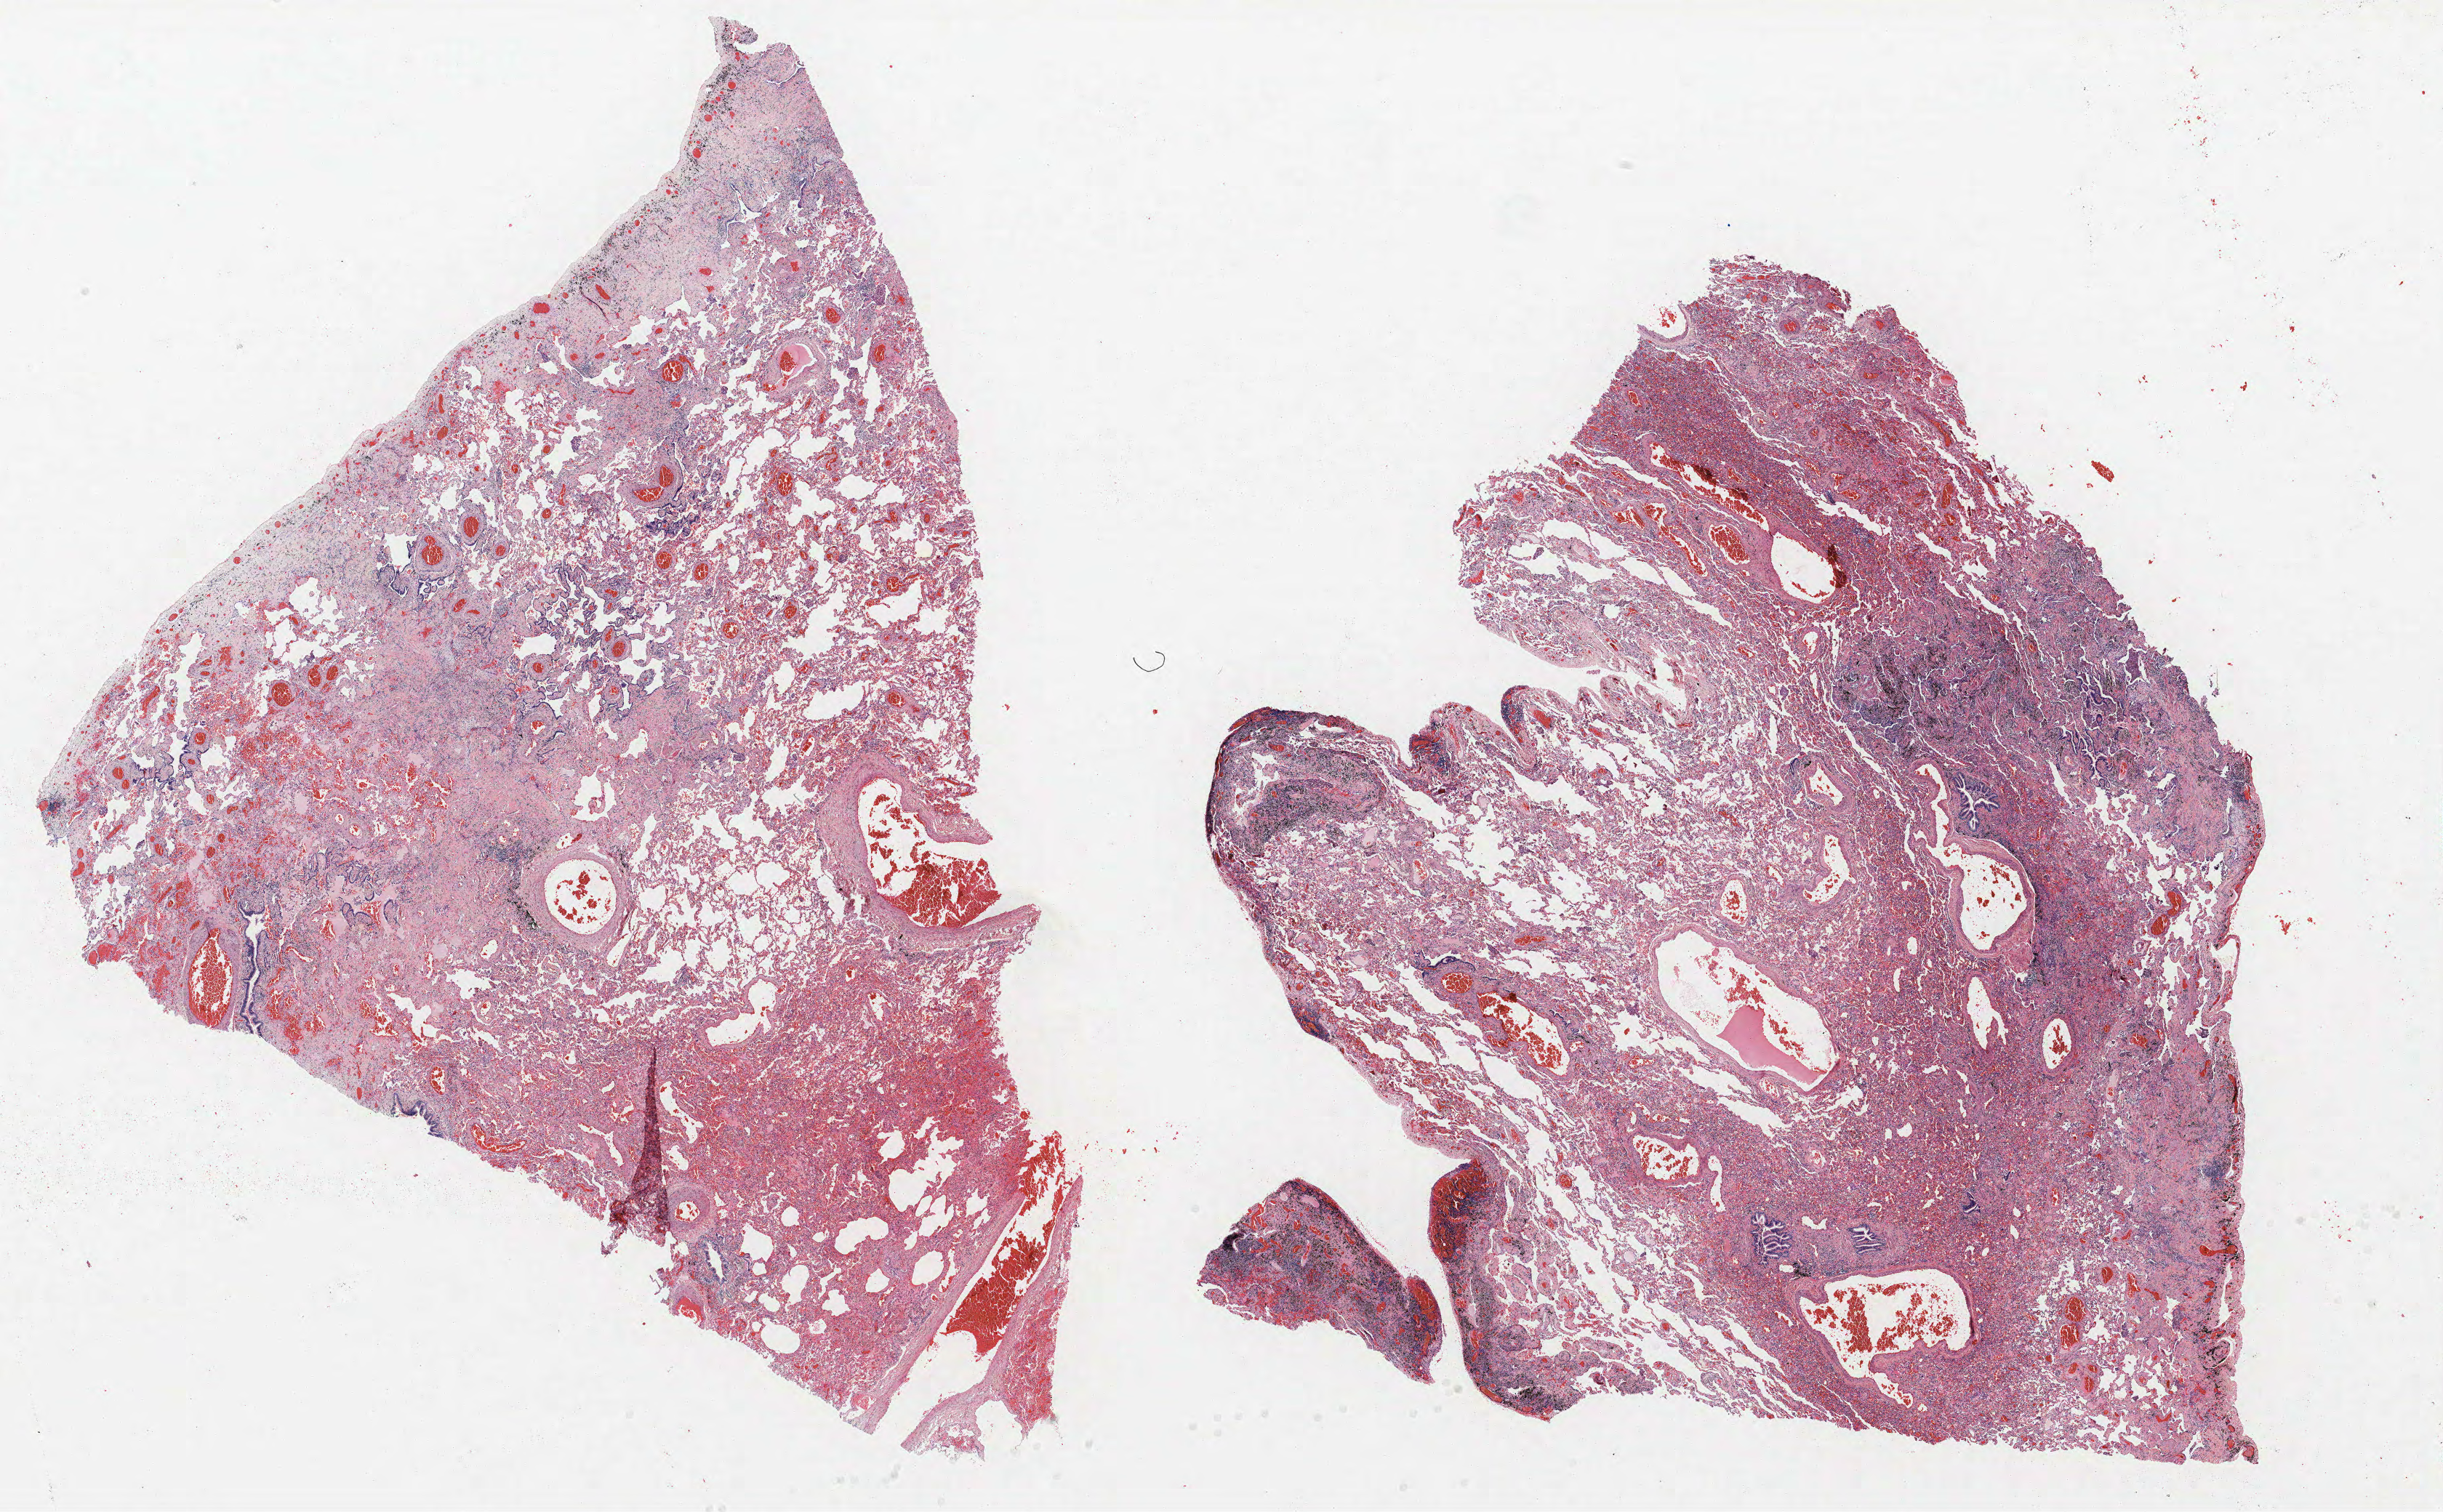
H&E-stained whole-slide image — a low-resolution overview of the entire scanned area, about 26.9 x 16.6 mm (slide scanned at 40x); FFPE section; lung tissue. Male, age 69 at enrolment. Grade: moderately differentiated (G2).
- ICD-O-3 topography: lower lobe of lung (C34.3)
- stage (AJCC 6th edition): IA
- tumour size (pathology): 25 mm
- primary tumour location (clinical record): right lower lobe
- participant's lung-cancer diagnosis: Squamous cell carcinoma, NOS (ICD-O-3 8070/3)